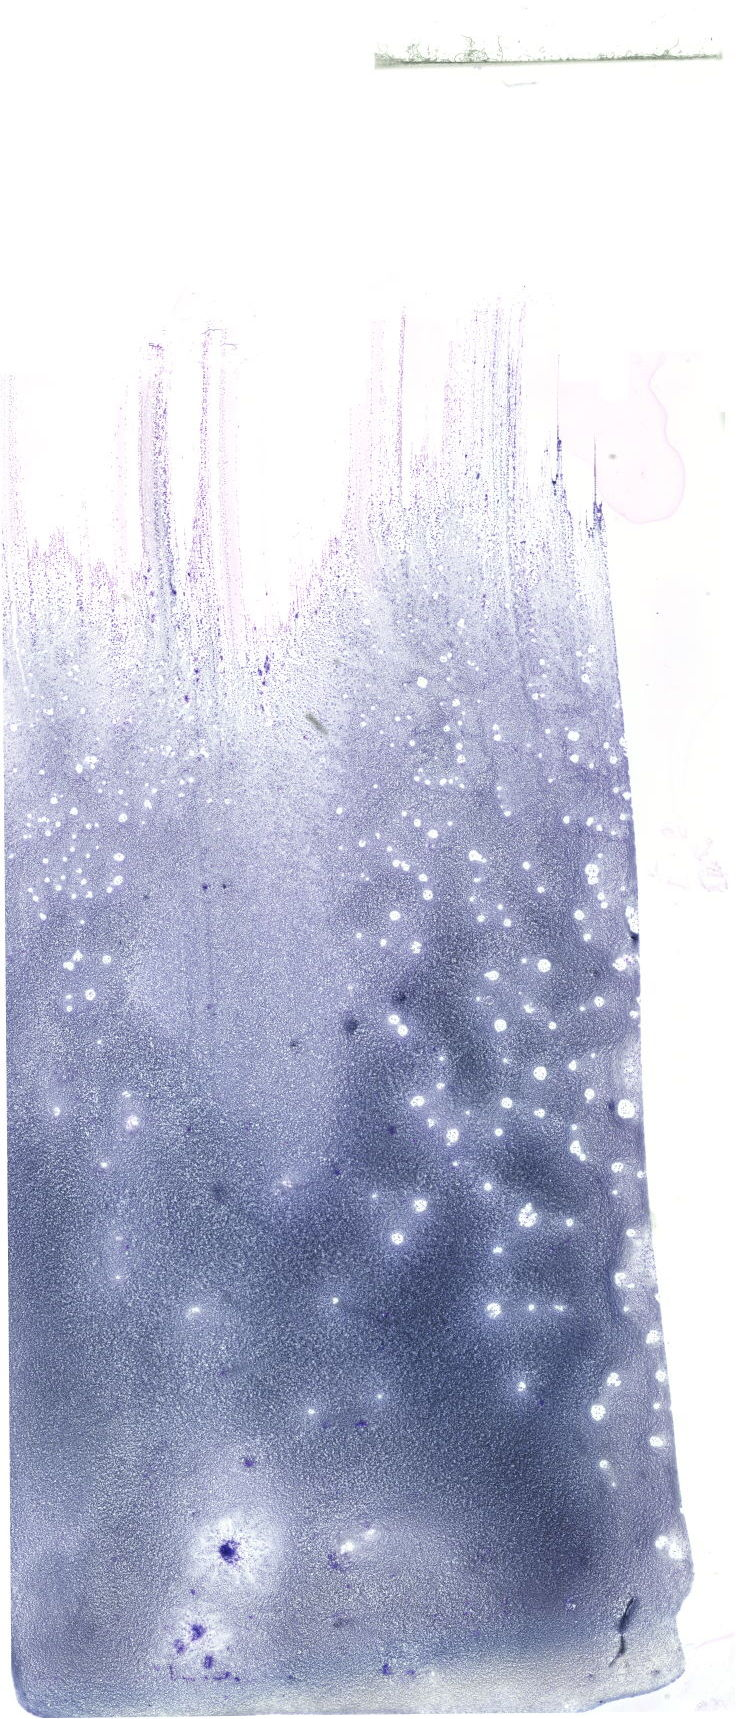
May-Grünwald–Giemsa-stained marrow aspirate smear (whole slide), whole scanned area (about 20.9 x 48.7 mm) shown as a low-resolution overview. Patient sex: male.
* diagnosis: Blast Phase Chronic Myeloid Leukemia, BCR-ABL1 Positive